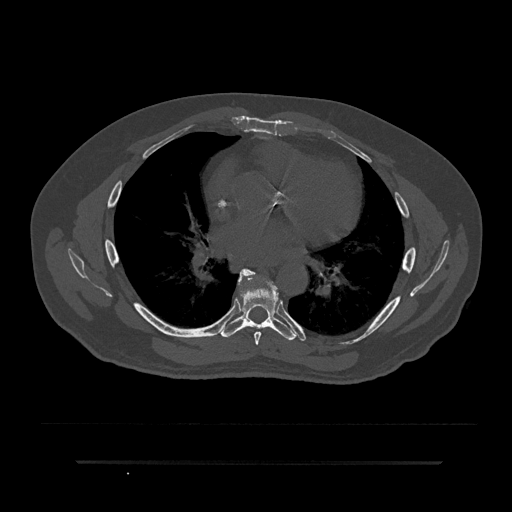
CT including the spine, one axial slice. Slice 497 of 797 in the series (ordered by position). 120 kVp. Bone window (W 1800 / L 400 HU). 512 × 512 image matrix, field of view 464 × 464 mm. Male patient, age 59 years. Case-level facts recorded for this patient, not image findings: primary cancer: bile ducts.
Outlined on this slice (semi-automatic segmentation, software-assisted and operator-edited):
- T6 vertebra: bounding box (x1, y1, x2, y2) in pixels: (238, 270, 261, 345)
- T7 vertebra: (221, 269, 296, 341)